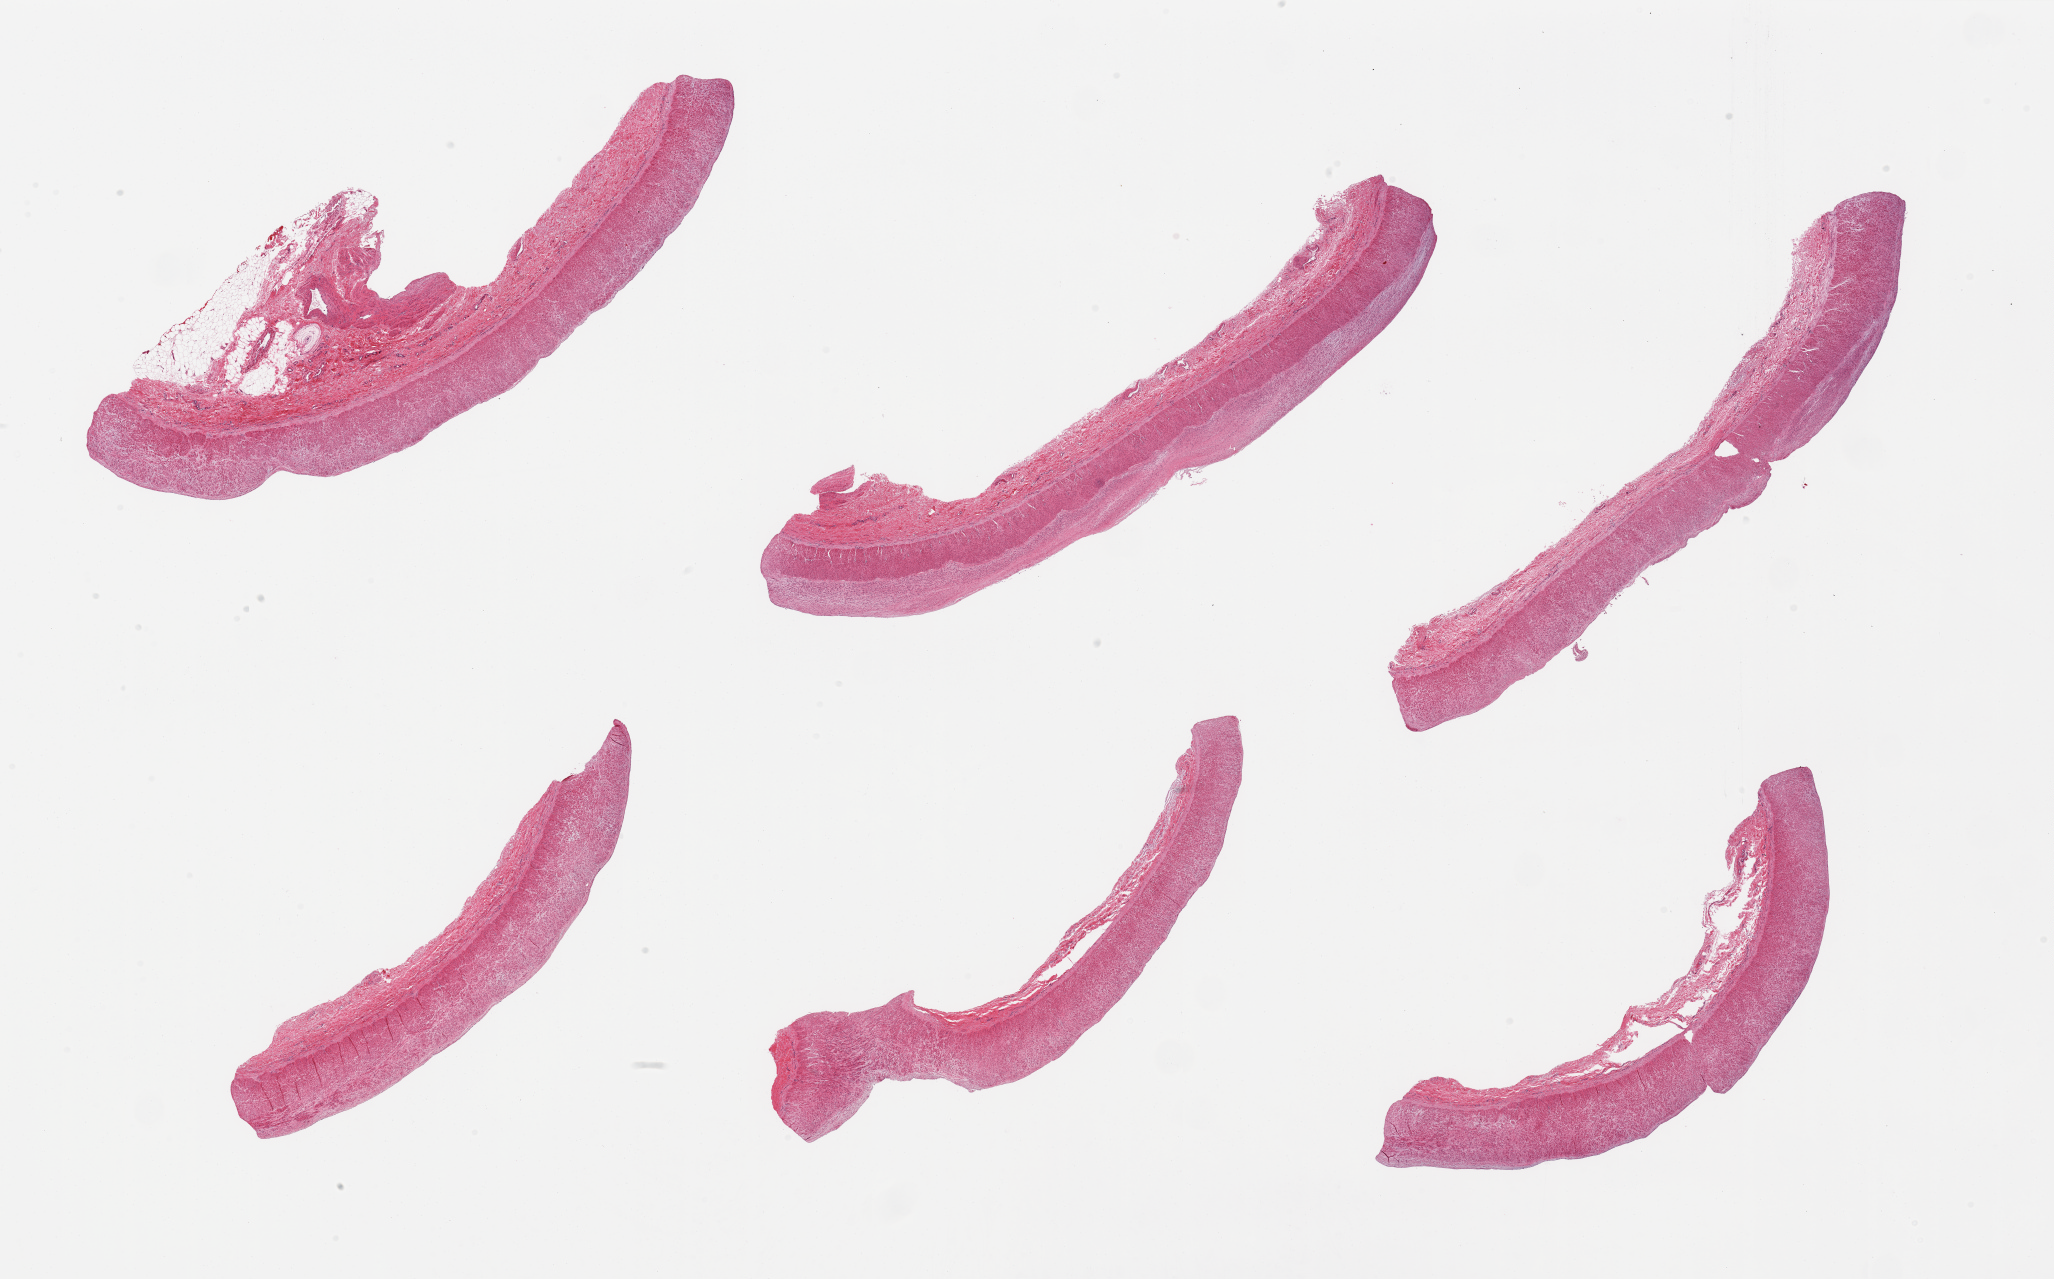
Haematoxylin and eosin whole-slide image, a low-resolution overview of the entire scanned area, about 32.5 x 20.2 mm, PAXgene-fixed, paraffin-embedded tissue, section of tibial artery (target tissue), donor tissue sample. Male donor.
Pathologist's review note for this sample: 6 pieces, large elastic artery (aorta), ~0.7mm atherosis.